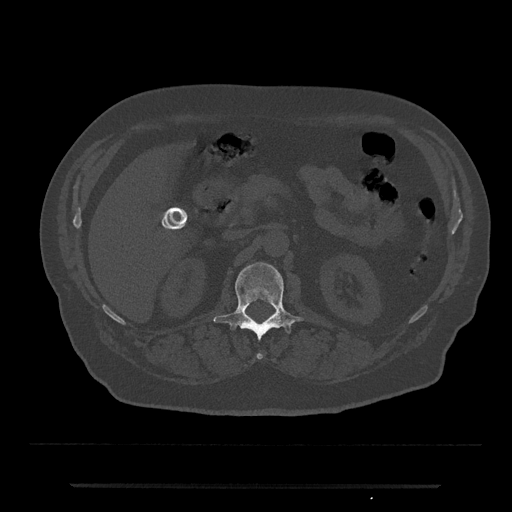
CT including the spine, one axial slice; position 536 of 797 along the scan axis; reconstruction kernel Br40s/3; 120 kVp; bone window (W 1800 / L 400 HU); 0.5 mm slice thickness; 512 × 512 image matrix, field of view 434 × 434 mm. Patient: male, 80 years. From the clinical record (not read from this slice): primary cancer: prostate.
Annotated regions visible in this slice (semi-automatically segmented with operator editing):
- L1 vertebra: bounding box [x1, y1, x2, y2] px = [214, 262, 303, 359]